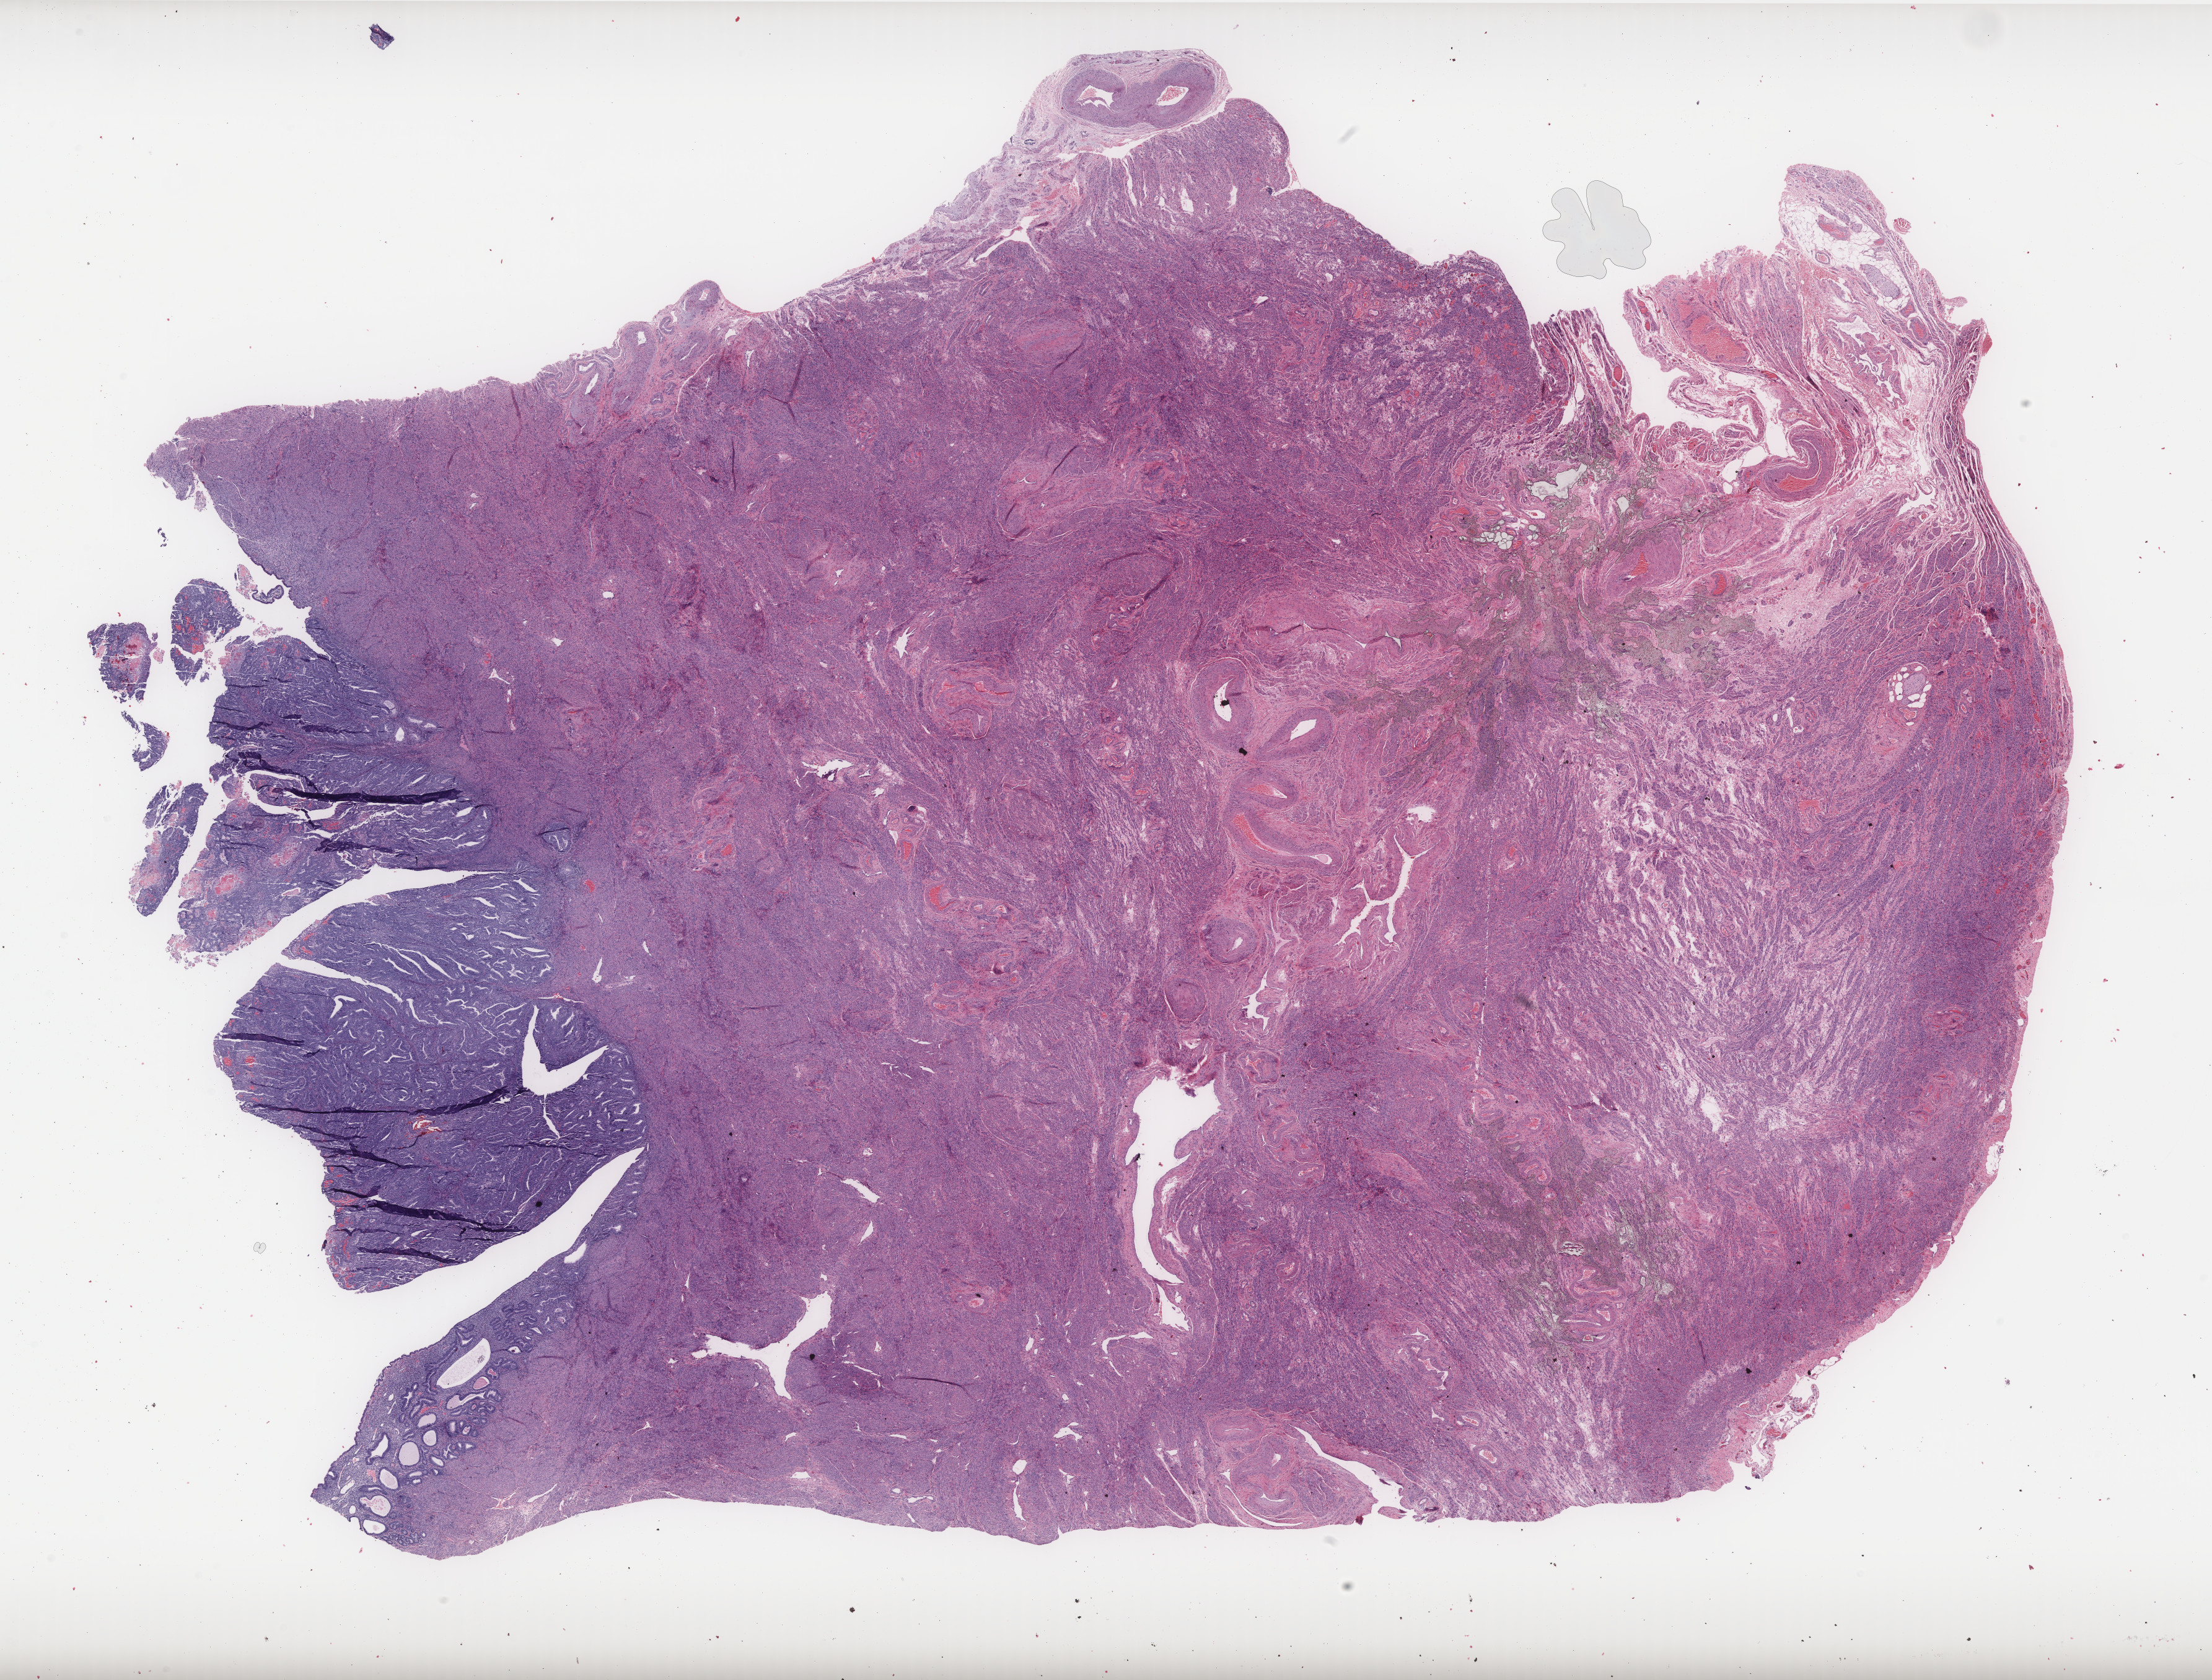
Whole-slide histology image, H&E — whole scanned area (about 28.6 x 21.7 mm, from a 40x scan) shown as a low-resolution overview. FFPE section. Sample: primary tumour, uterus. Female patient; age at initial diagnosis 83 years. Histologic grade: G2 (moderately differentiated).
Diagnosis: Endometrioid adenocarcinoma, NOS (endometrium). FIGO stage: IA. Lymph nodes positive (case pathology): 0 of 13 examined.